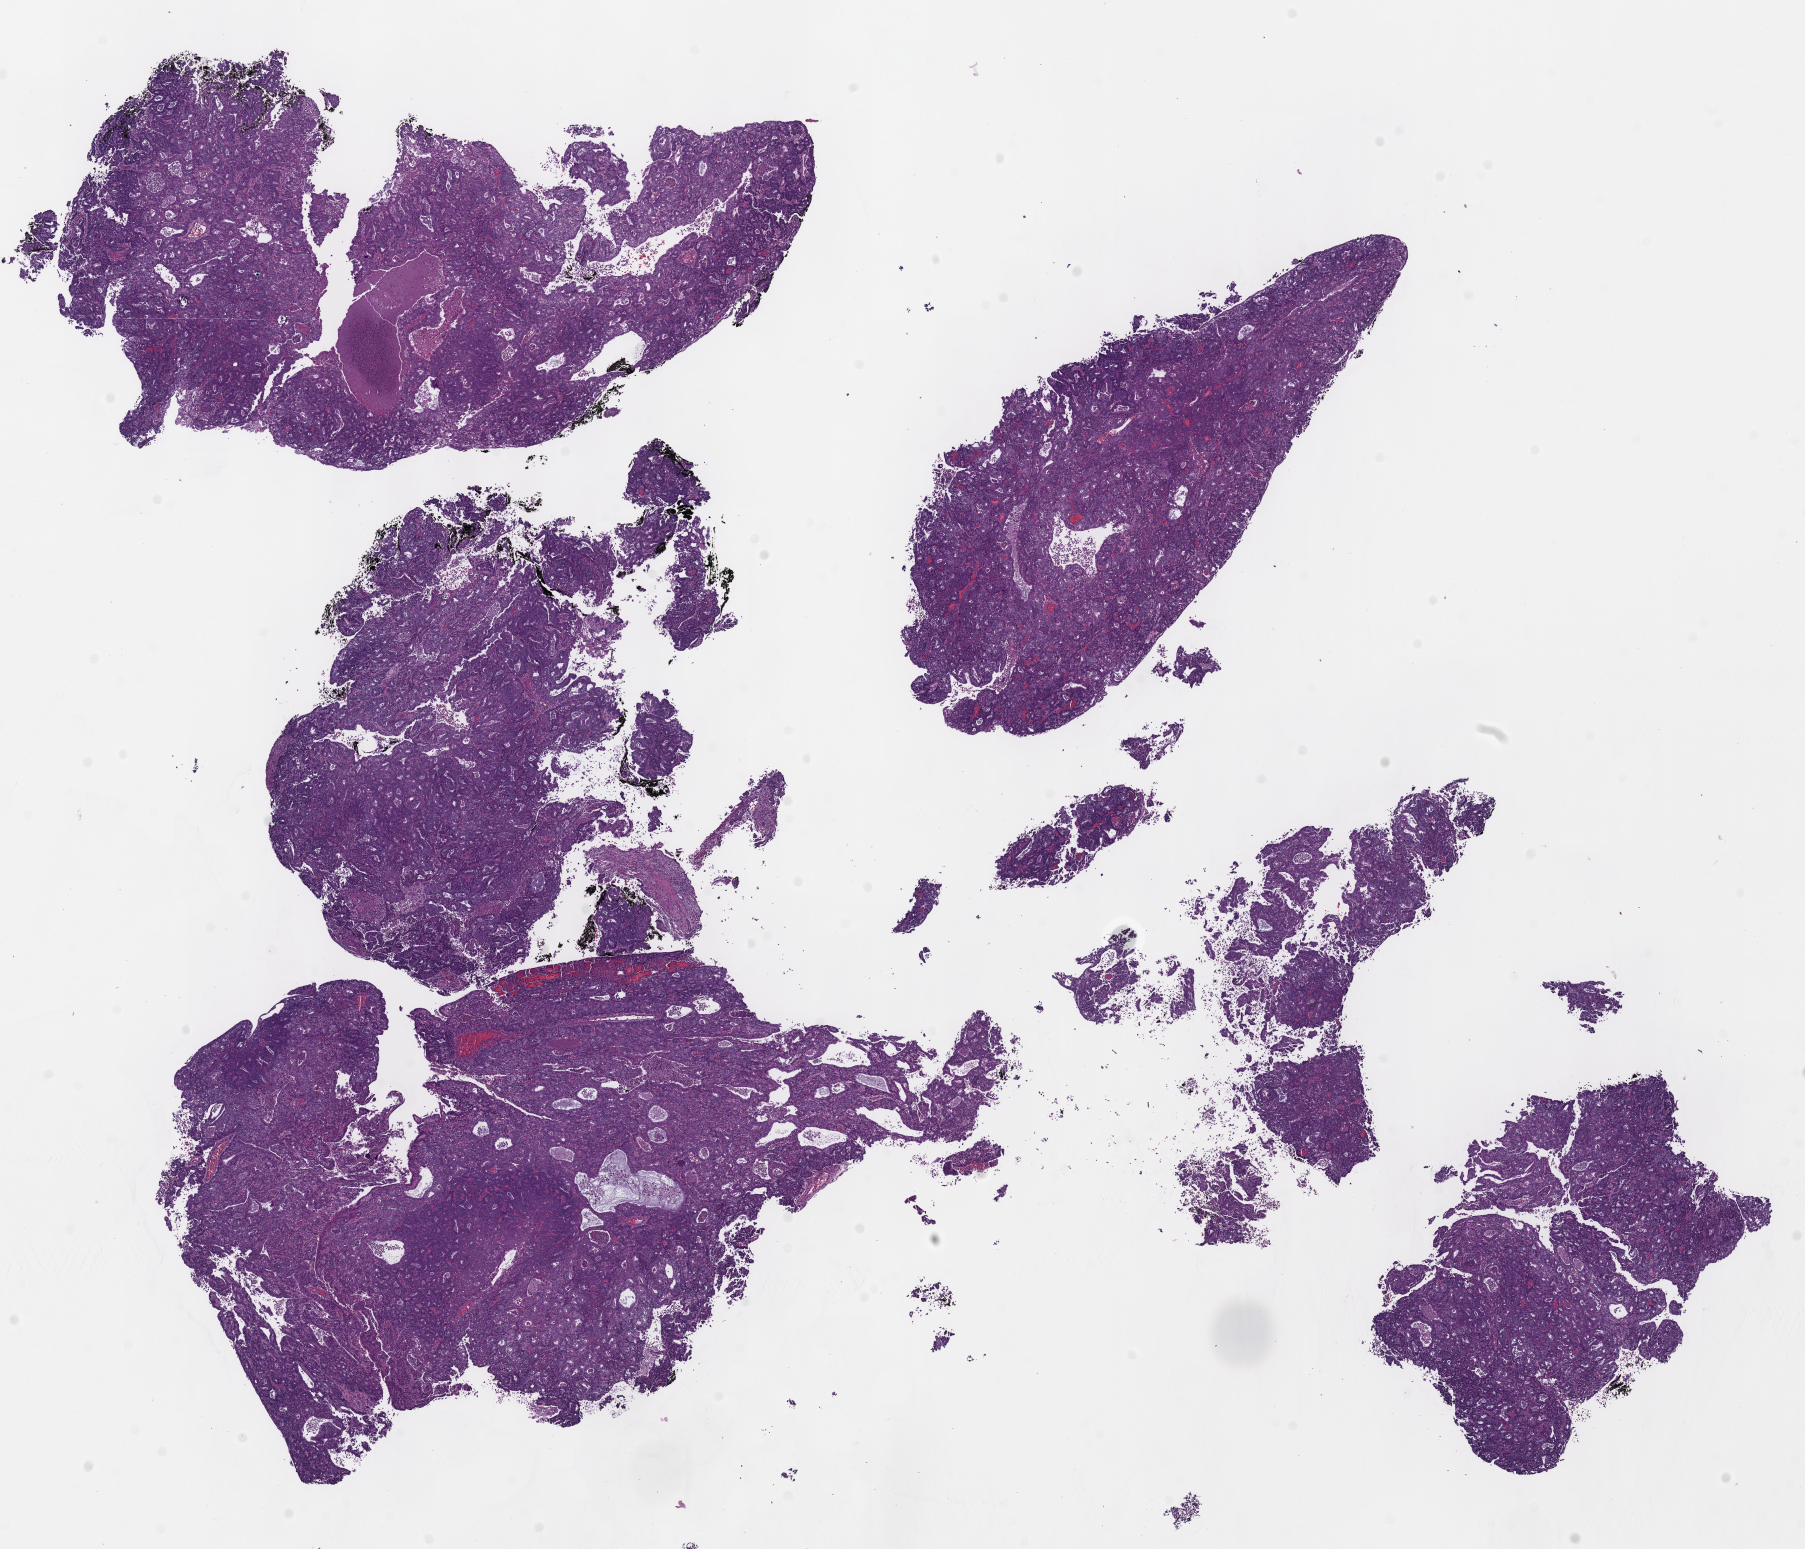
Digitized H&E-stained tissue section (whole slide) — a low-resolution overview of the entire scanned area, about 14.2 x 12.2 mm (slide scanned at 40x), FFPE section, sample: primary tumour, uterus. Female patient; age at initial diagnosis 63 years. Histologic grade: G3 (poorly differentiated).
• histologic diagnosis: Endometrioid adenocarcinoma, NOS (endometrium)
• FIGO stage: IA